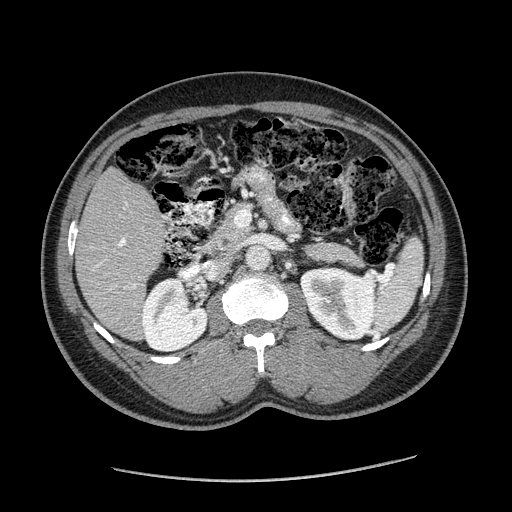
Contrast-enhanced abdominal CT (liver protocol), one axial slice. Slice 75 of 182 in the series (ordered by position). 120 kVp. Soft-tissue window (W 400 / L 40 HU). 512 × 512 image matrix. From the clinical record (not read from this slice): diagnosis: hepatocellular carcinoma (patient treated with transarterial chemoembolisation; whether this scan precedes or follows treatment is not stated here); TNM stage (as recorded): Stage-I; Child-Pugh class: A.
Outlined on this slice (semi-automatic segmentation, software-assisted and operator-edited):
- liver parenchyma outside the tumour (the mass and vessels are separate outlines, so this box may not span the whole liver): bounding box (x1, y1, x2, y2) in pixels: (76, 168, 166, 339)
- liver vessels: (96, 238, 136, 288)